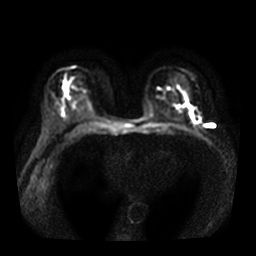
Breast MRI, one axial slice. Diffusion-weighted series; image 2 of 4 stored at this slice position (different b-values; order by instance number). 3 T. 256 × 256 image matrix. Female patient.
Outlined on this slice (expert manual segmentation):
- tumour on diffusion-weighted imaging: bounding box (x1, y1, x2, y2) in pixels: (190, 106, 201, 123)